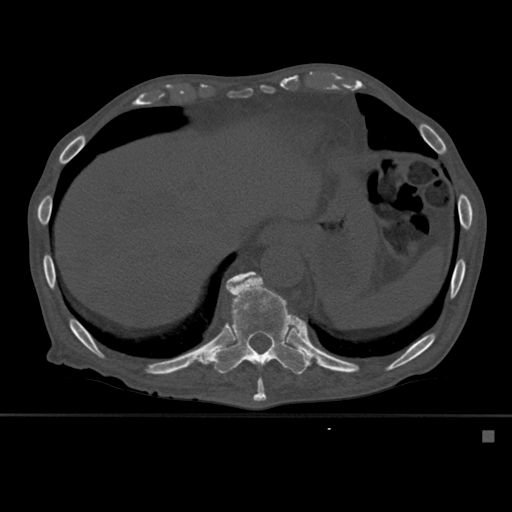
CT including the spine, one axial slice. Slice 301 of 527 in the series (ordered by position). Bone window (W 1800 / L 400 HU). 1.5 mm slice thickness. 512 × 512 image matrix. Male patient, age 78 years. From the clinical record (not read from this slice): primary cancer: prostate.
Annotated regions visible in this slice (semi-automatic segmentation, software-assisted and operator-edited):
- T10 vertebra: box from (x=231, y=272) to (x=267, y=401) px
- T11 vertebra: (x=204, y=271)–(x=312, y=375)